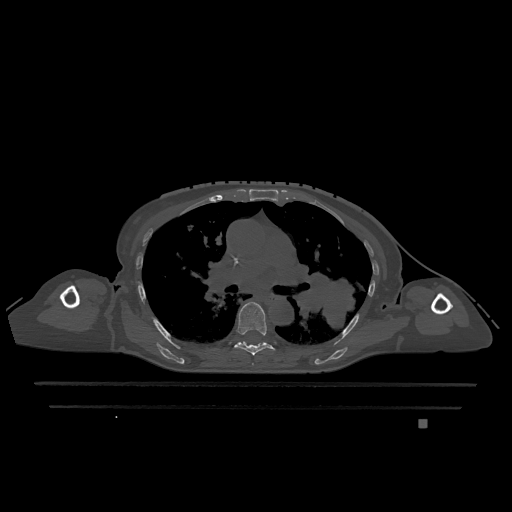
CT including the spine, one axial slice; position 786 of 1317 along the scan axis; bone window (W 1800 / L 400 HU); 512 × 512 image matrix, field of view 500 × 500 mm. Female patient, age 74 years. Case-level facts recorded for this patient, not image findings: primary cancer: lung; vertebrae with lytic lesions (as recorded): T1, T4, T5, T6, L4, L5.
Structures marked on this image (semi-automatic segmentation, software-assisted and operator-edited):
- T6 vertebra: bounding box <234,302,275,355> (left, top, right, bottom; pixels)